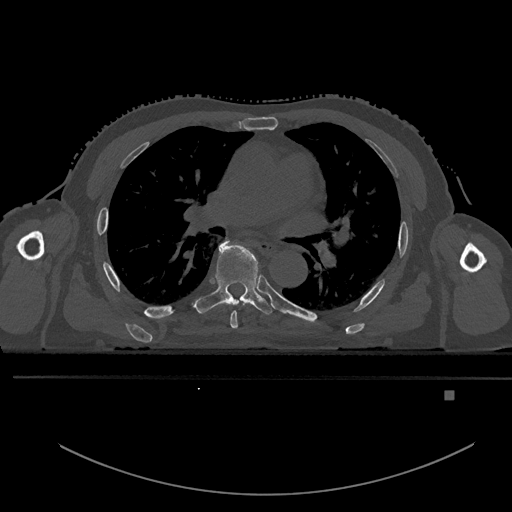
CT including the spine, one axial slice. Position 322 of 969 along the scan axis. Bone window (W 1800 / L 400 HU). 0.5 mm slice thickness. 512 × 512 image matrix, field of view 456 × 456 mm. Patient: male, 82 years. Case-level facts recorded for this patient, not image findings: primary cancer: prostate; vertebrae with lytic lesions (as recorded): T11, T9, T8, T2.
Structures marked on this image (semi-automatic segmentation, software-assisted and operator-edited):
- T5 vertebra: box from (x=229, y=242) to (x=238, y=329) px
- T6 vertebra: (x=192, y=238)–(x=274, y=315)